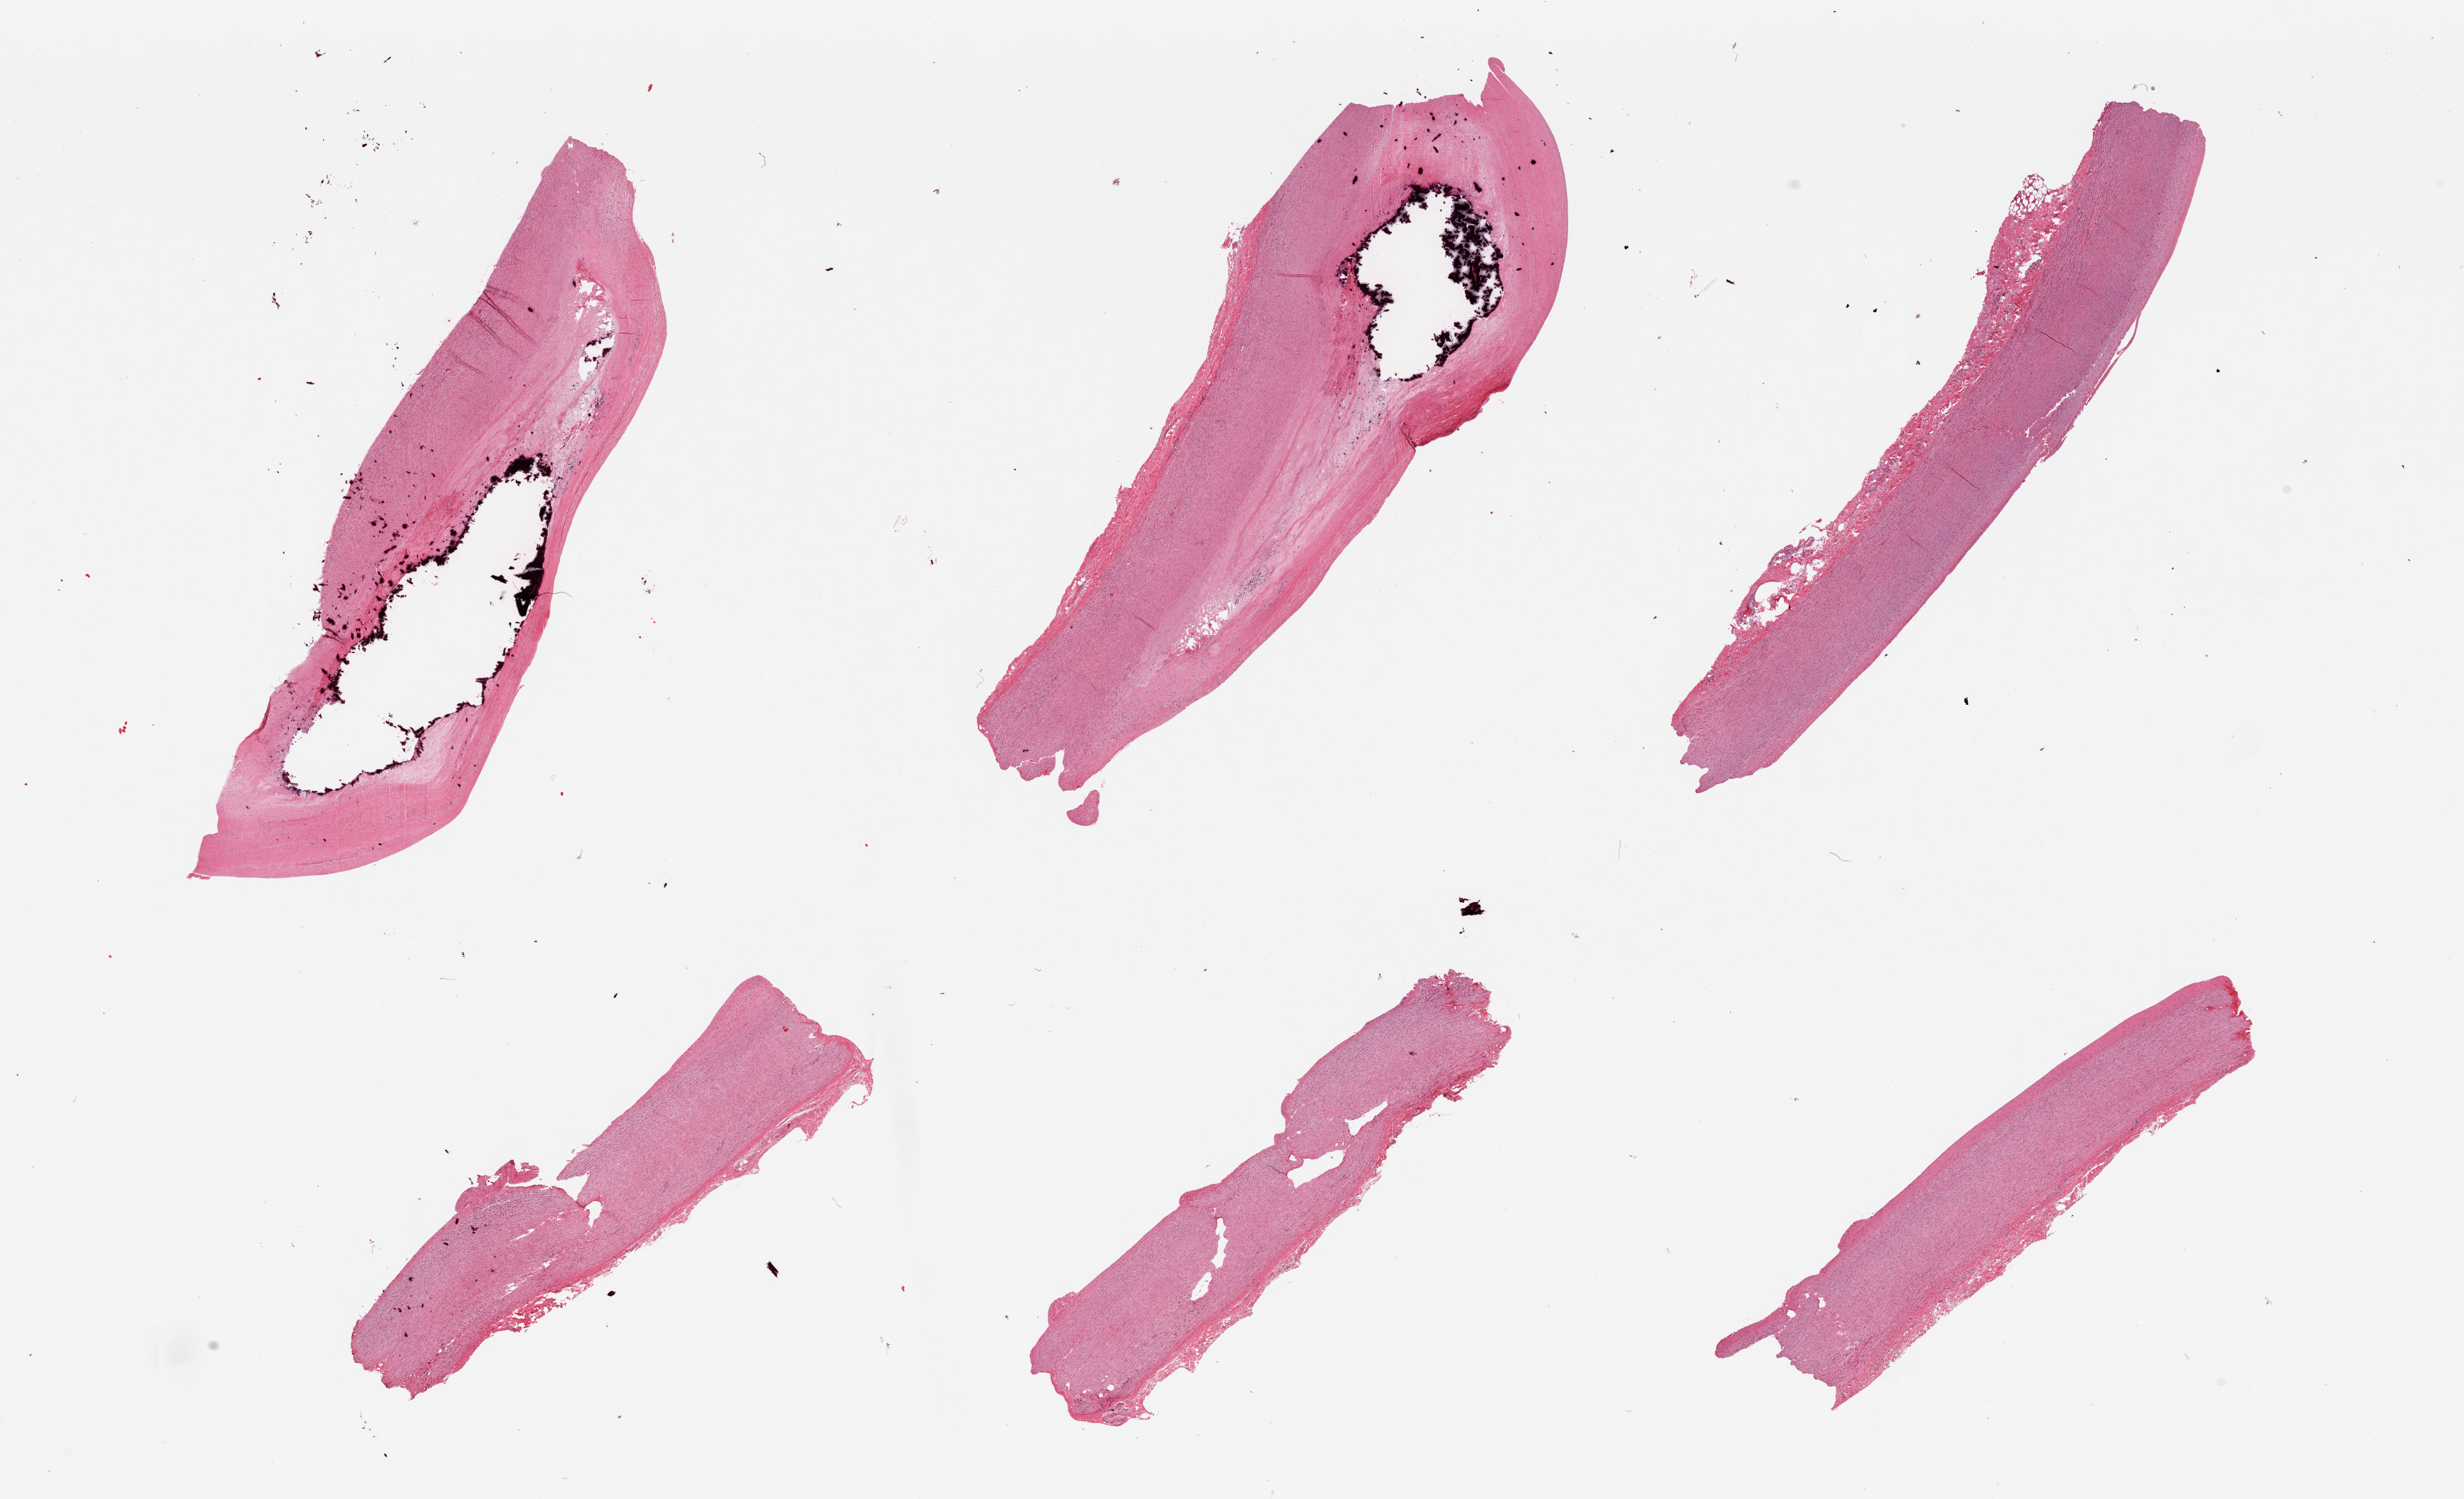
Whole-slide image, hematoxylin and eosin (H&E) stain, brightfield — low-resolution overview of the scanned area, about 30.5 x 18.6 mm (from a 20x scan), PAXgene-fixed paraffin-embedded (PFPE) section, sampled site (target tissue): aorta, donor tissue sample.
Review note (as recorded): 6 pieces; severe calcific atherosclerosis.